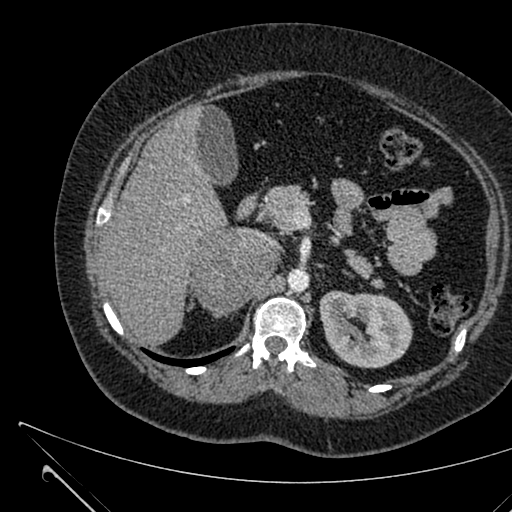
Contrast-enhanced abdominal CT, one axial slice. Slice 407 of 731 in the series (ordered by position). Intravenous contrast given. Soft-tissue window (W 400 / L 40 HU). 512 × 512 image matrix, field of view 376 × 376 mm. Female patient, age 36 years. Case-level facts recorded for this patient, not image findings: diagnosis: adrenocortical carcinoma; tumour side: right adrenal; tumour size at pathology: 10 cm.
Annotated regions visible in this slice (semi-automatic segmentation, software-assisted and operator-edited):
- mass: box from (x=191, y=232) to (x=273, y=314) px